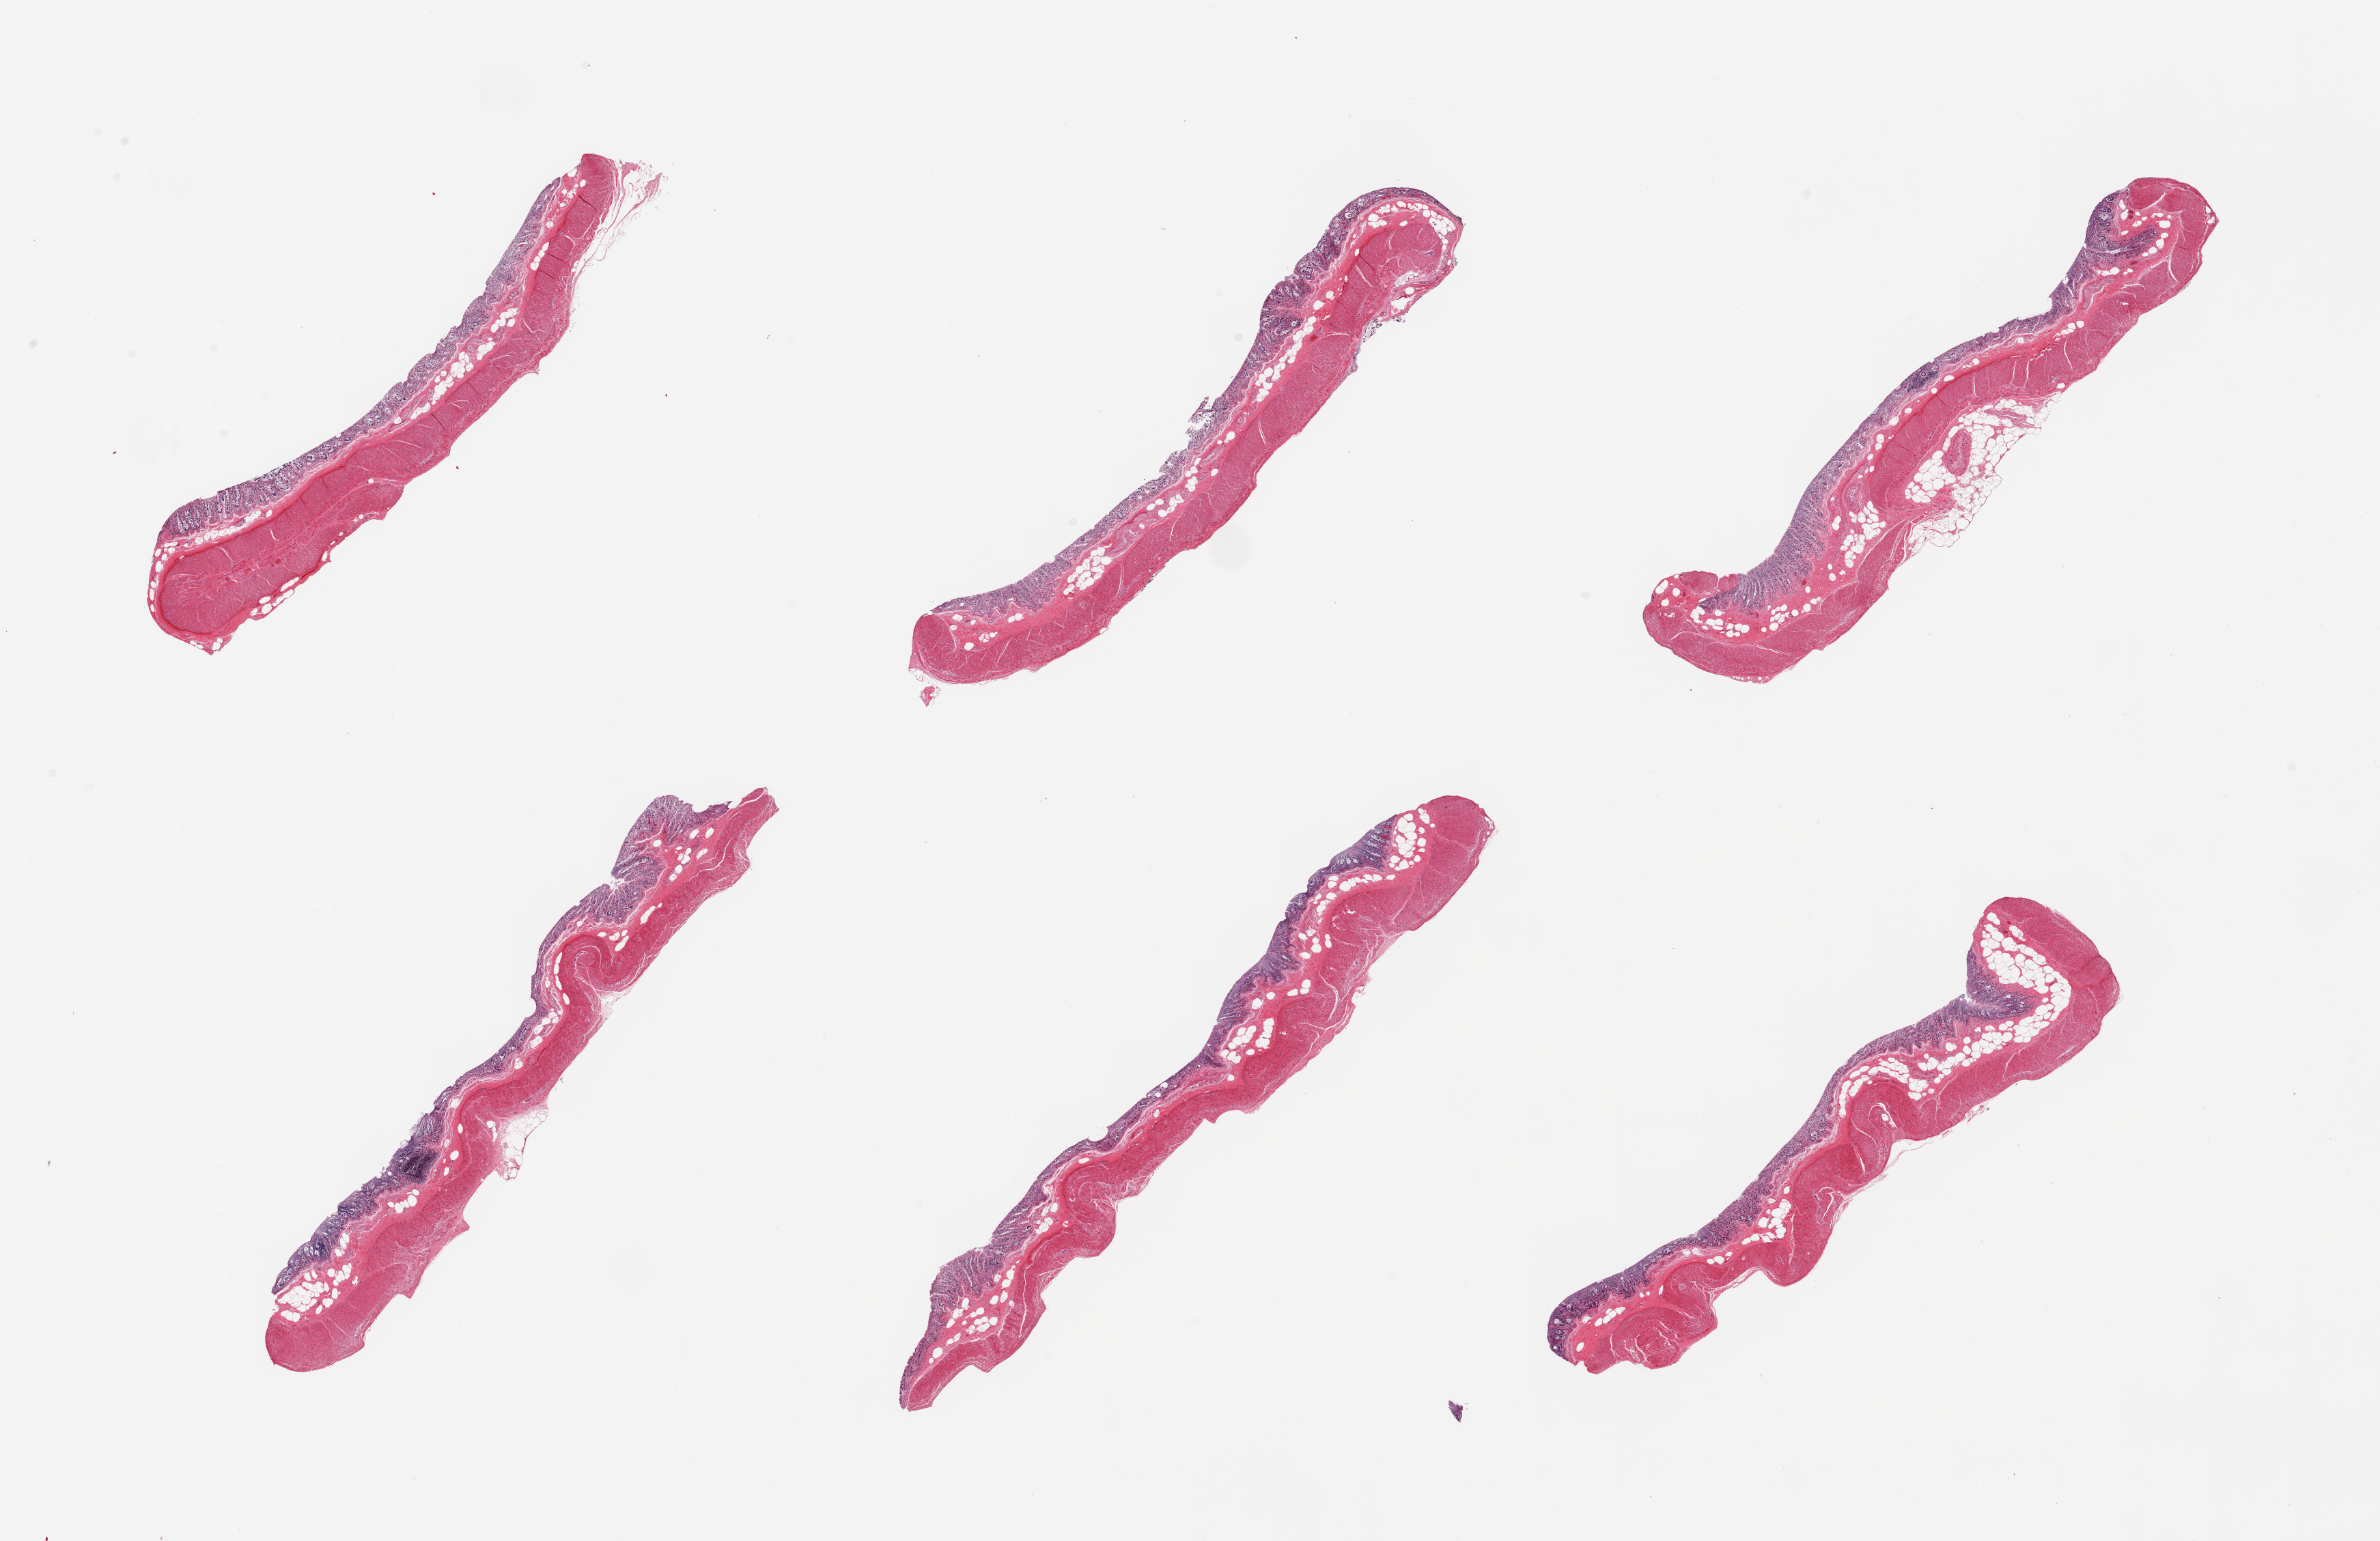
Hematoxylin and eosin (H&E) whole-slide image, low-resolution overview of the scanned area, about 27.6 x 17.9 mm (slide scanned at 20x); PAXgene-fixed, paraffin-embedded tissue; section of transverse colon (target tissue); donor tissue sample. Male donor.
• reviewer comment on this tissue sample: 6 pieces; full thickness sections, mucosa is autolyzed